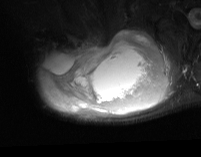
MRI of an extremity soft-tissue mass, one axial slice; slice 47 of 74 in the series (ordered by position); STIR; MR volume resampled by the dataset authors to the PET/CT grid (not the native acquisition matrix); 3.27 mm slice thickness; 201 × 157 image matrix, field of view 196 × 153 mm. Male patient. From the clinical record (not read from this slice): histological type: pleiomorphic spindle cell undifferentiated; grade: high; site of the primary tumour: right parascapusular.
Annotated regions visible in this slice (expert contour drawn on MRI and transferred to this co-registered scan by the dataset authors):
- gross tumour volume including surrounding oedema: bounding box (x1, y1, x2, y2) in pixels: (39, 27, 178, 119)
- gross tumour volume (mass): (42, 29, 168, 115)